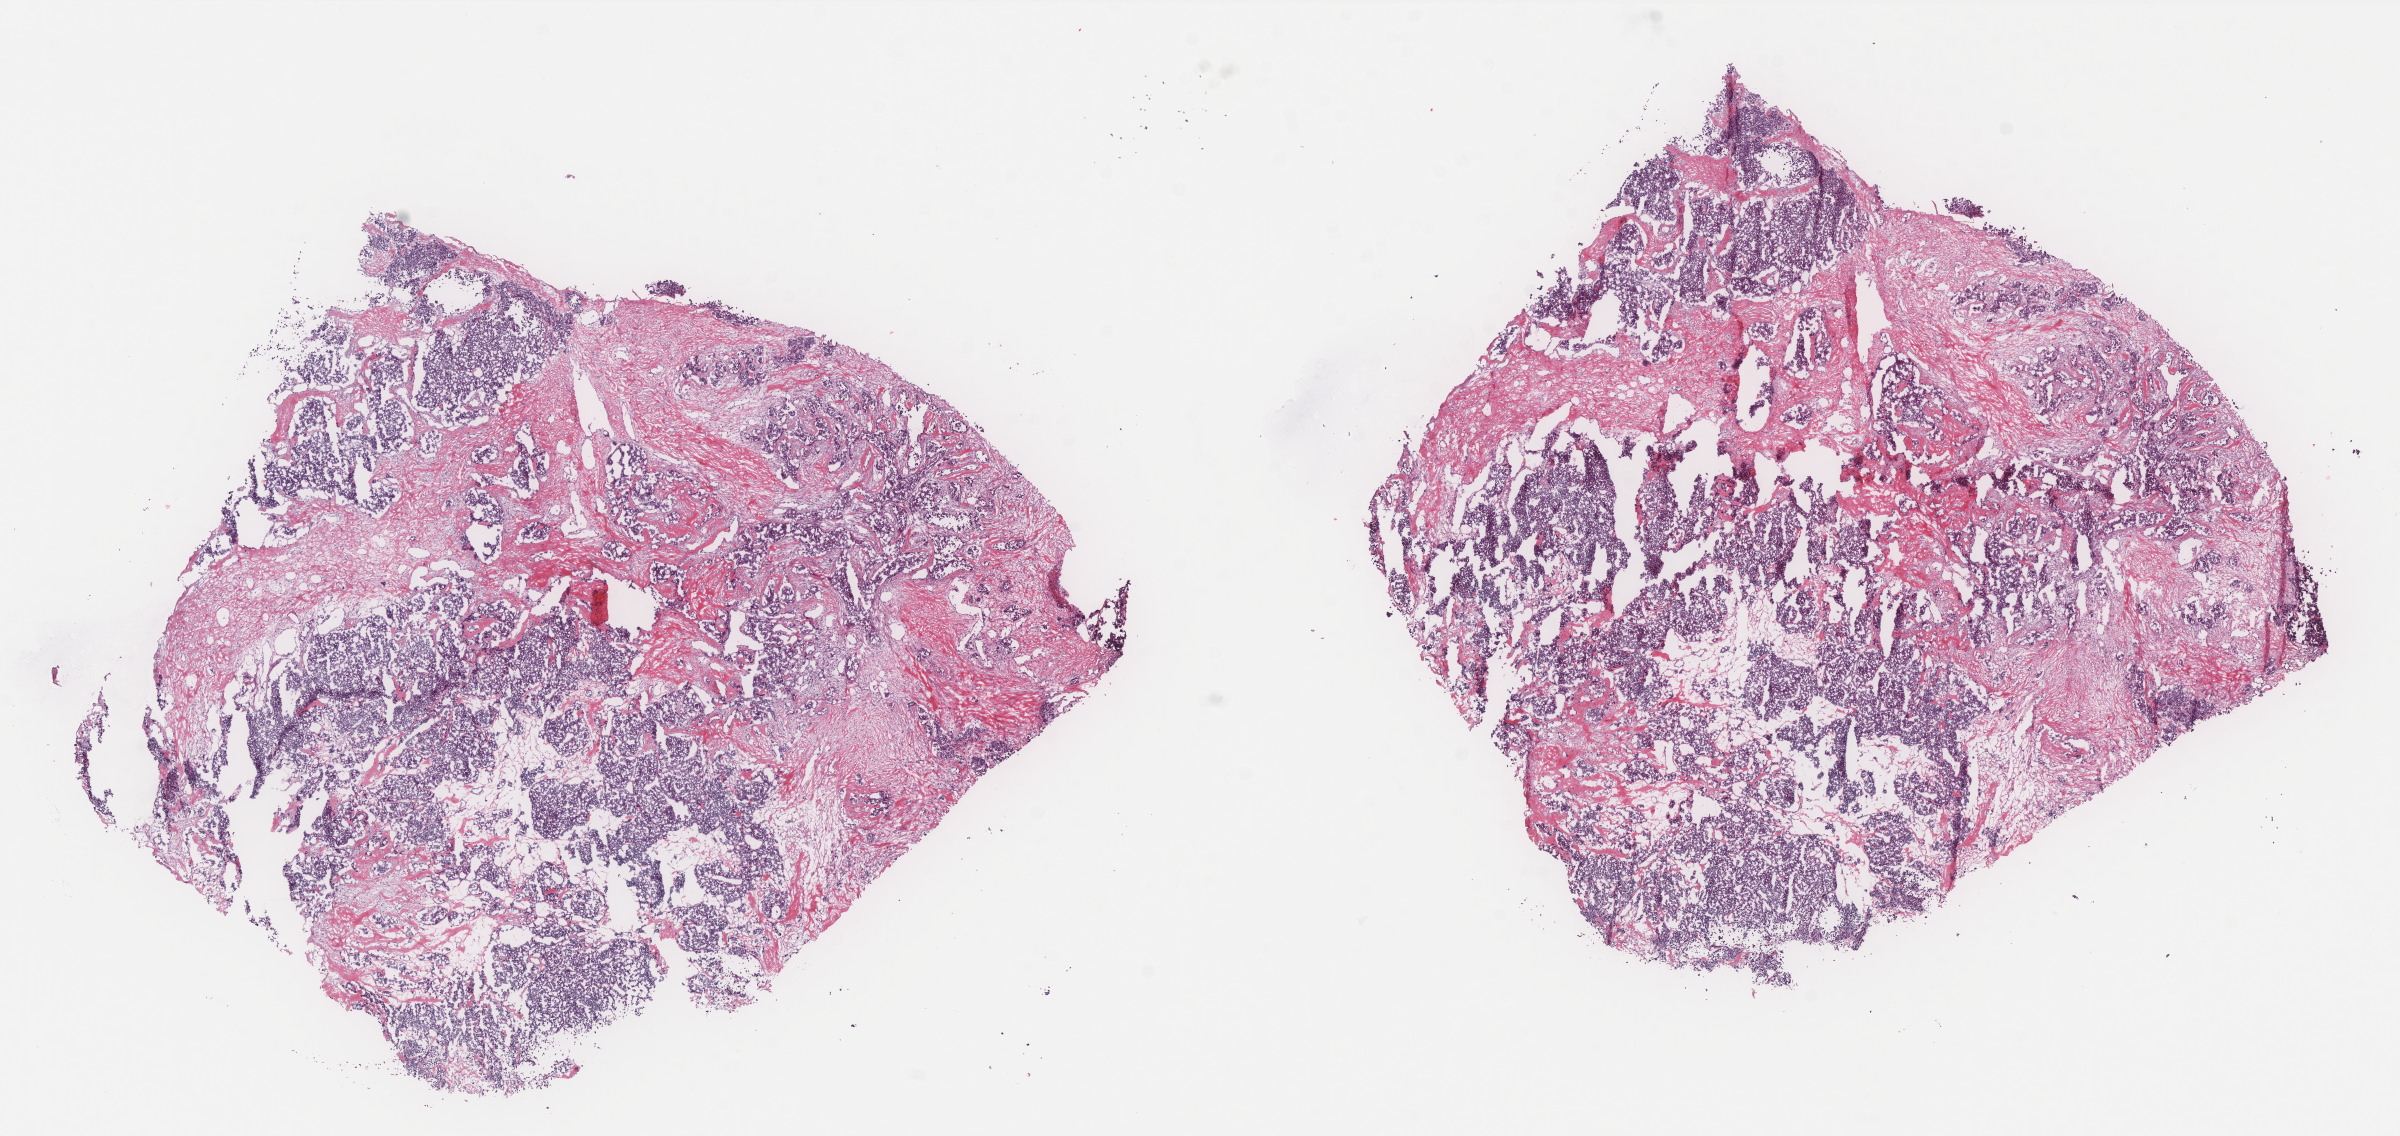
Hematoxylin and eosin (H&E) stained whole-slide image, a low-resolution overview of the entire scanned area, about 19.2 x 9.1 mm (slide scanned at 40x). Frozen section. Breast, primary tumour sample. Female patient; age at initial diagnosis 62 years. Composition of this section per pathologist review: tumour cells 85%, tumour nuclei 90%.
Histologic diagnosis: Infiltrating duct carcinoma, NOS.